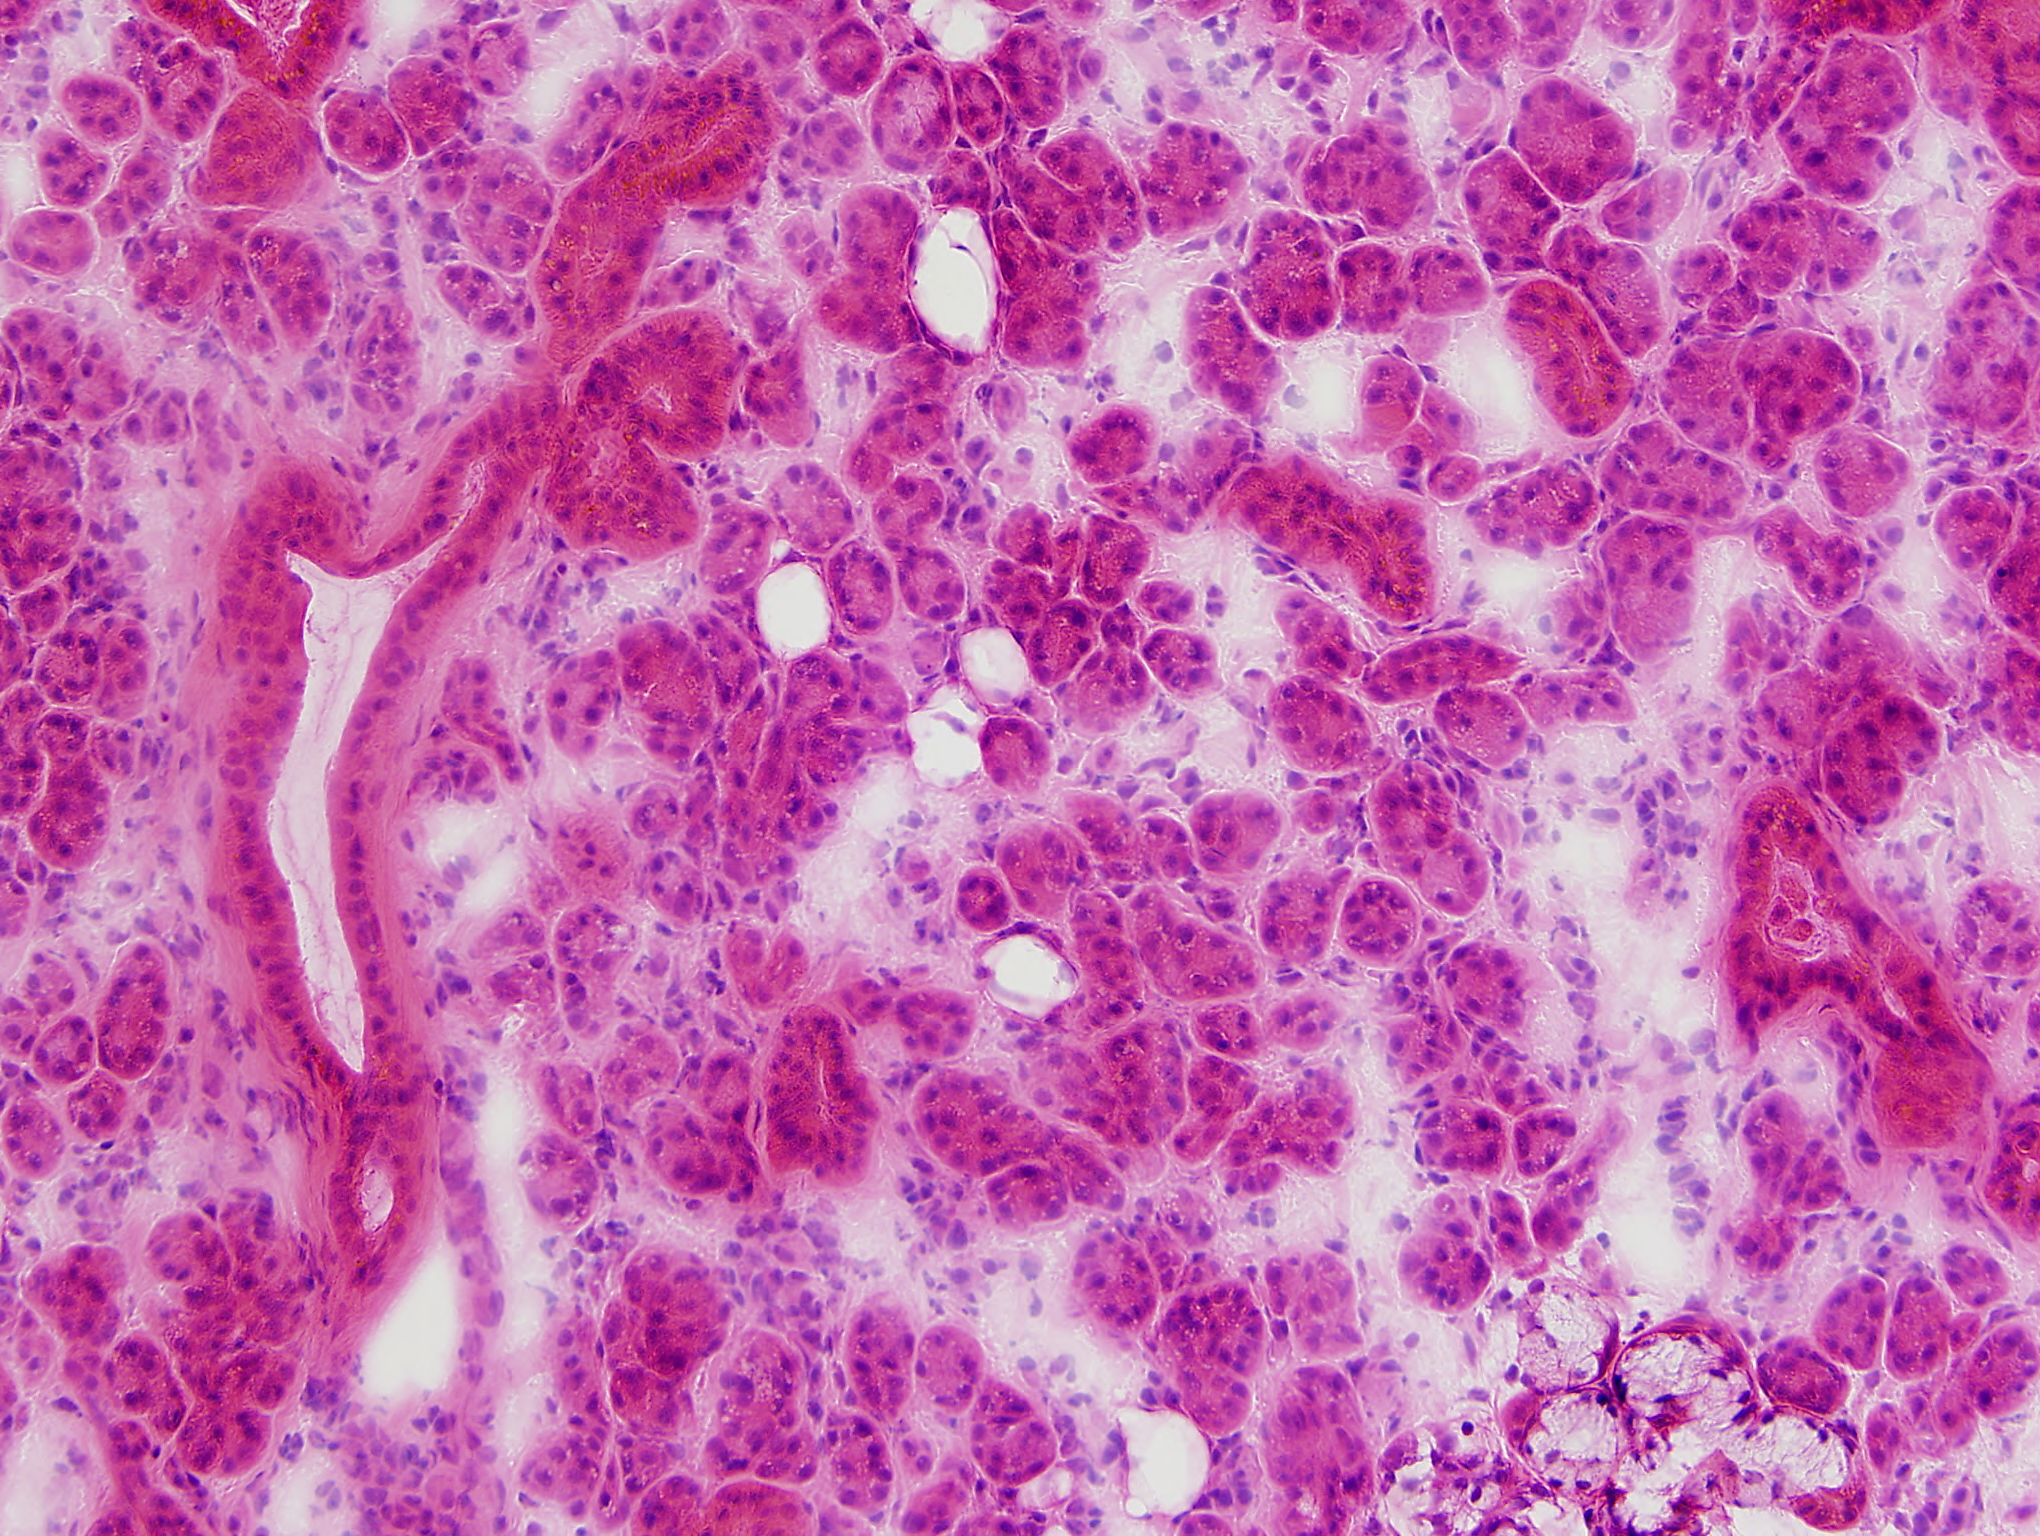
H&E-stained micrograph of a single small tissue field — roughly 1.0 x 0.8 mm in extent. Frozen section. Sample: solid tissue normal (non-tumour tissue), head and neck. Patient: male, age at initial diagnosis 79 years.
This section: solid tissue normal (non-tumour) sample from the same patient. Patient diagnosis: Squamous cell carcinoma, NOS.